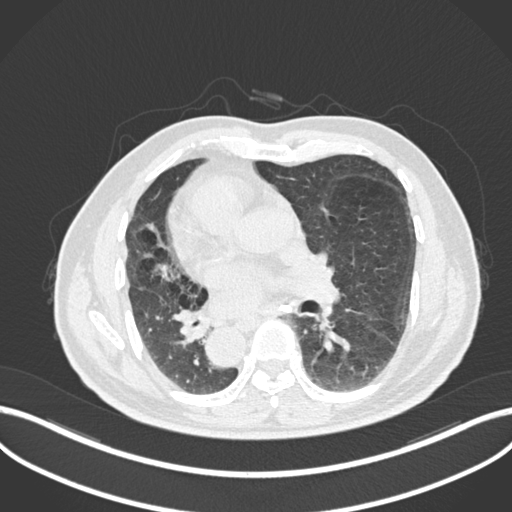
Chest CT, one axial slice; slice 108 of 206 in the series (ordered by position); reconstruction kernel B30f; lung window (W 1500 / L -600 HU); 1 mm slice thickness; 512 × 512 image matrix, field of view 400 × 400 mm. Male patient, age 67 years. Case-level facts recorded for this patient, not image findings: clinical TNM (as recorded): T2a N0 M0.
Outlined on this slice (bounding box drawn by a radiologist):
- lung tumour (recorded histology: squamous cell carcinoma): bounding box (x1, y1, x2, y2) in pixels: (171, 303, 209, 343)